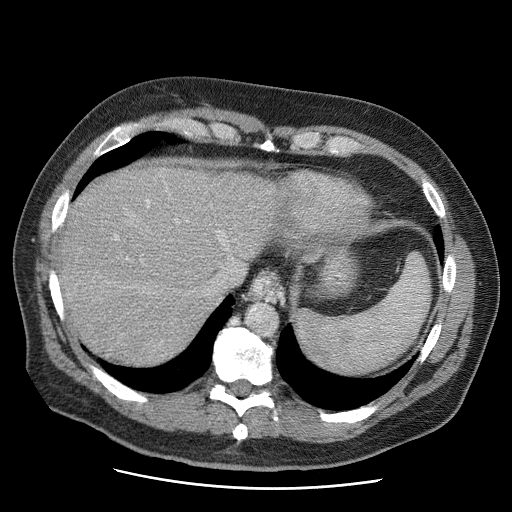
Contrast-enhanced abdominal CT (liver protocol), one axial slice. Slice 49 of 81 in the series (ordered by position). Reconstruction kernel STANDARD. 120 kVp. Soft-tissue window (W 400 / L 40 HU). 2.5 mm slice thickness. 512 × 512 image matrix, field of view 380 × 380 mm. From the clinical record (not read from this slice): diagnosis: hepatocellular carcinoma (patient treated with transarterial chemoembolisation; whether this scan precedes or follows treatment is not stated here); TNM stage (as recorded): Stage-IIIA; Child-Pugh class: A; tumour differentiation: moderately differentiated; tumour nodularity: multinodular.
Structures marked on this image (semi-automatic segmentation, software-assisted and operator-edited):
- liver parenchyma outside the tumour (the mass and vessels are separate outlines, so this box may not span the whole liver): bounding box <56,164,284,364> (left, top, right, bottom; pixels)
- liver vessels: <146,200,224,236>